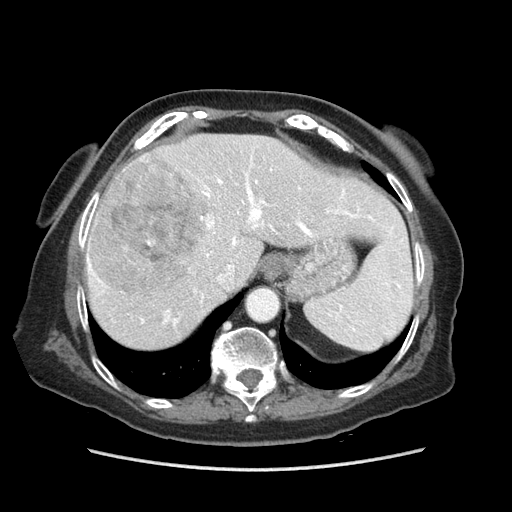
Contrast-enhanced abdominal CT (liver protocol), one axial slice. Reconstruction kernel STANDARD. 140 kVp. Soft-tissue window (W 400 / L 40 HU). 2.5 mm slice thickness. 512 × 512 image matrix. Case-level facts recorded for this patient, not image findings: diagnosis: hepatocellular carcinoma (patient treated with transarterial chemoembolisation; whether this scan precedes or follows treatment is not stated here); TNM stage (as recorded): Stage-IIIA; Child-Pugh class: A; tumour differentiation: well differentiated; tumour nodularity: multinodular.
Annotated regions visible in this slice (semi-automatic segmentation, software-assisted and operator-edited):
- abdominal aorta: bounding box <247,289,278,319> (left, top, right, bottom; pixels)
- liver parenchyma outside the tumour (the mass and vessels are separate outlines, so this box may not span the whole liver): <82,134,406,348>
- mass: <90,156,213,293>
- liver vessels: <84,156,403,326>